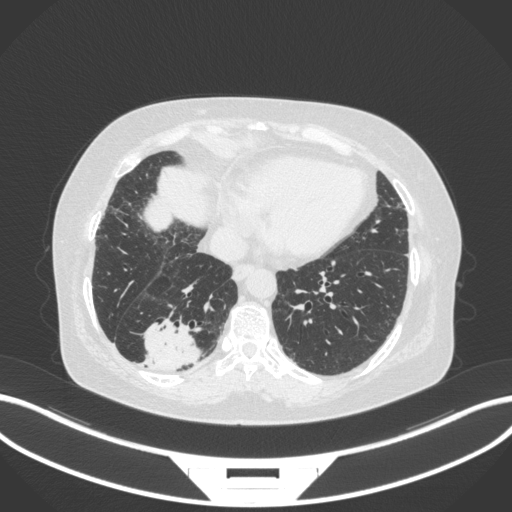
Chest CT, one axial slice; slice 65 of 303 in the series (ordered by position); reconstruction kernel B31f; 120 kVp; lung window (W 1500 / L -600 HU); 1 mm slice thickness; 512 × 512 image matrix. Female patient, age 65 years. Case-level facts recorded for this patient, not image findings: clinical TNM (as recorded): T2b N1 M0.
Outlined on this slice (rectangle marked by the reading radiologist):
- lung tumour (recorded histology: adenocarcinoma): bounding box <130,319,203,370> (left, top, right, bottom; pixels)